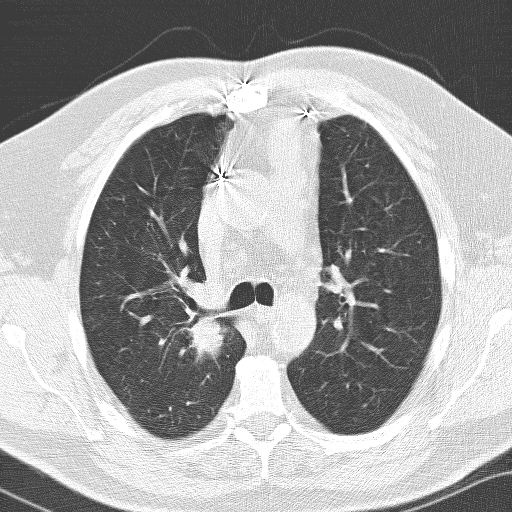
Low-dose screening chest CT, one axial slice; position 101 of 141 along the scan axis; lung window (W 1500 / L -600 HU); 3.2 mm slice thickness; 512 × 512 image matrix.
Annotated regions visible in this slice (manually delineated by an expert):
- lesion 1 (tumor, upper lobe of right lung): bounding box (x1, y1, x2, y2) in pixels: (190, 318, 224, 360)